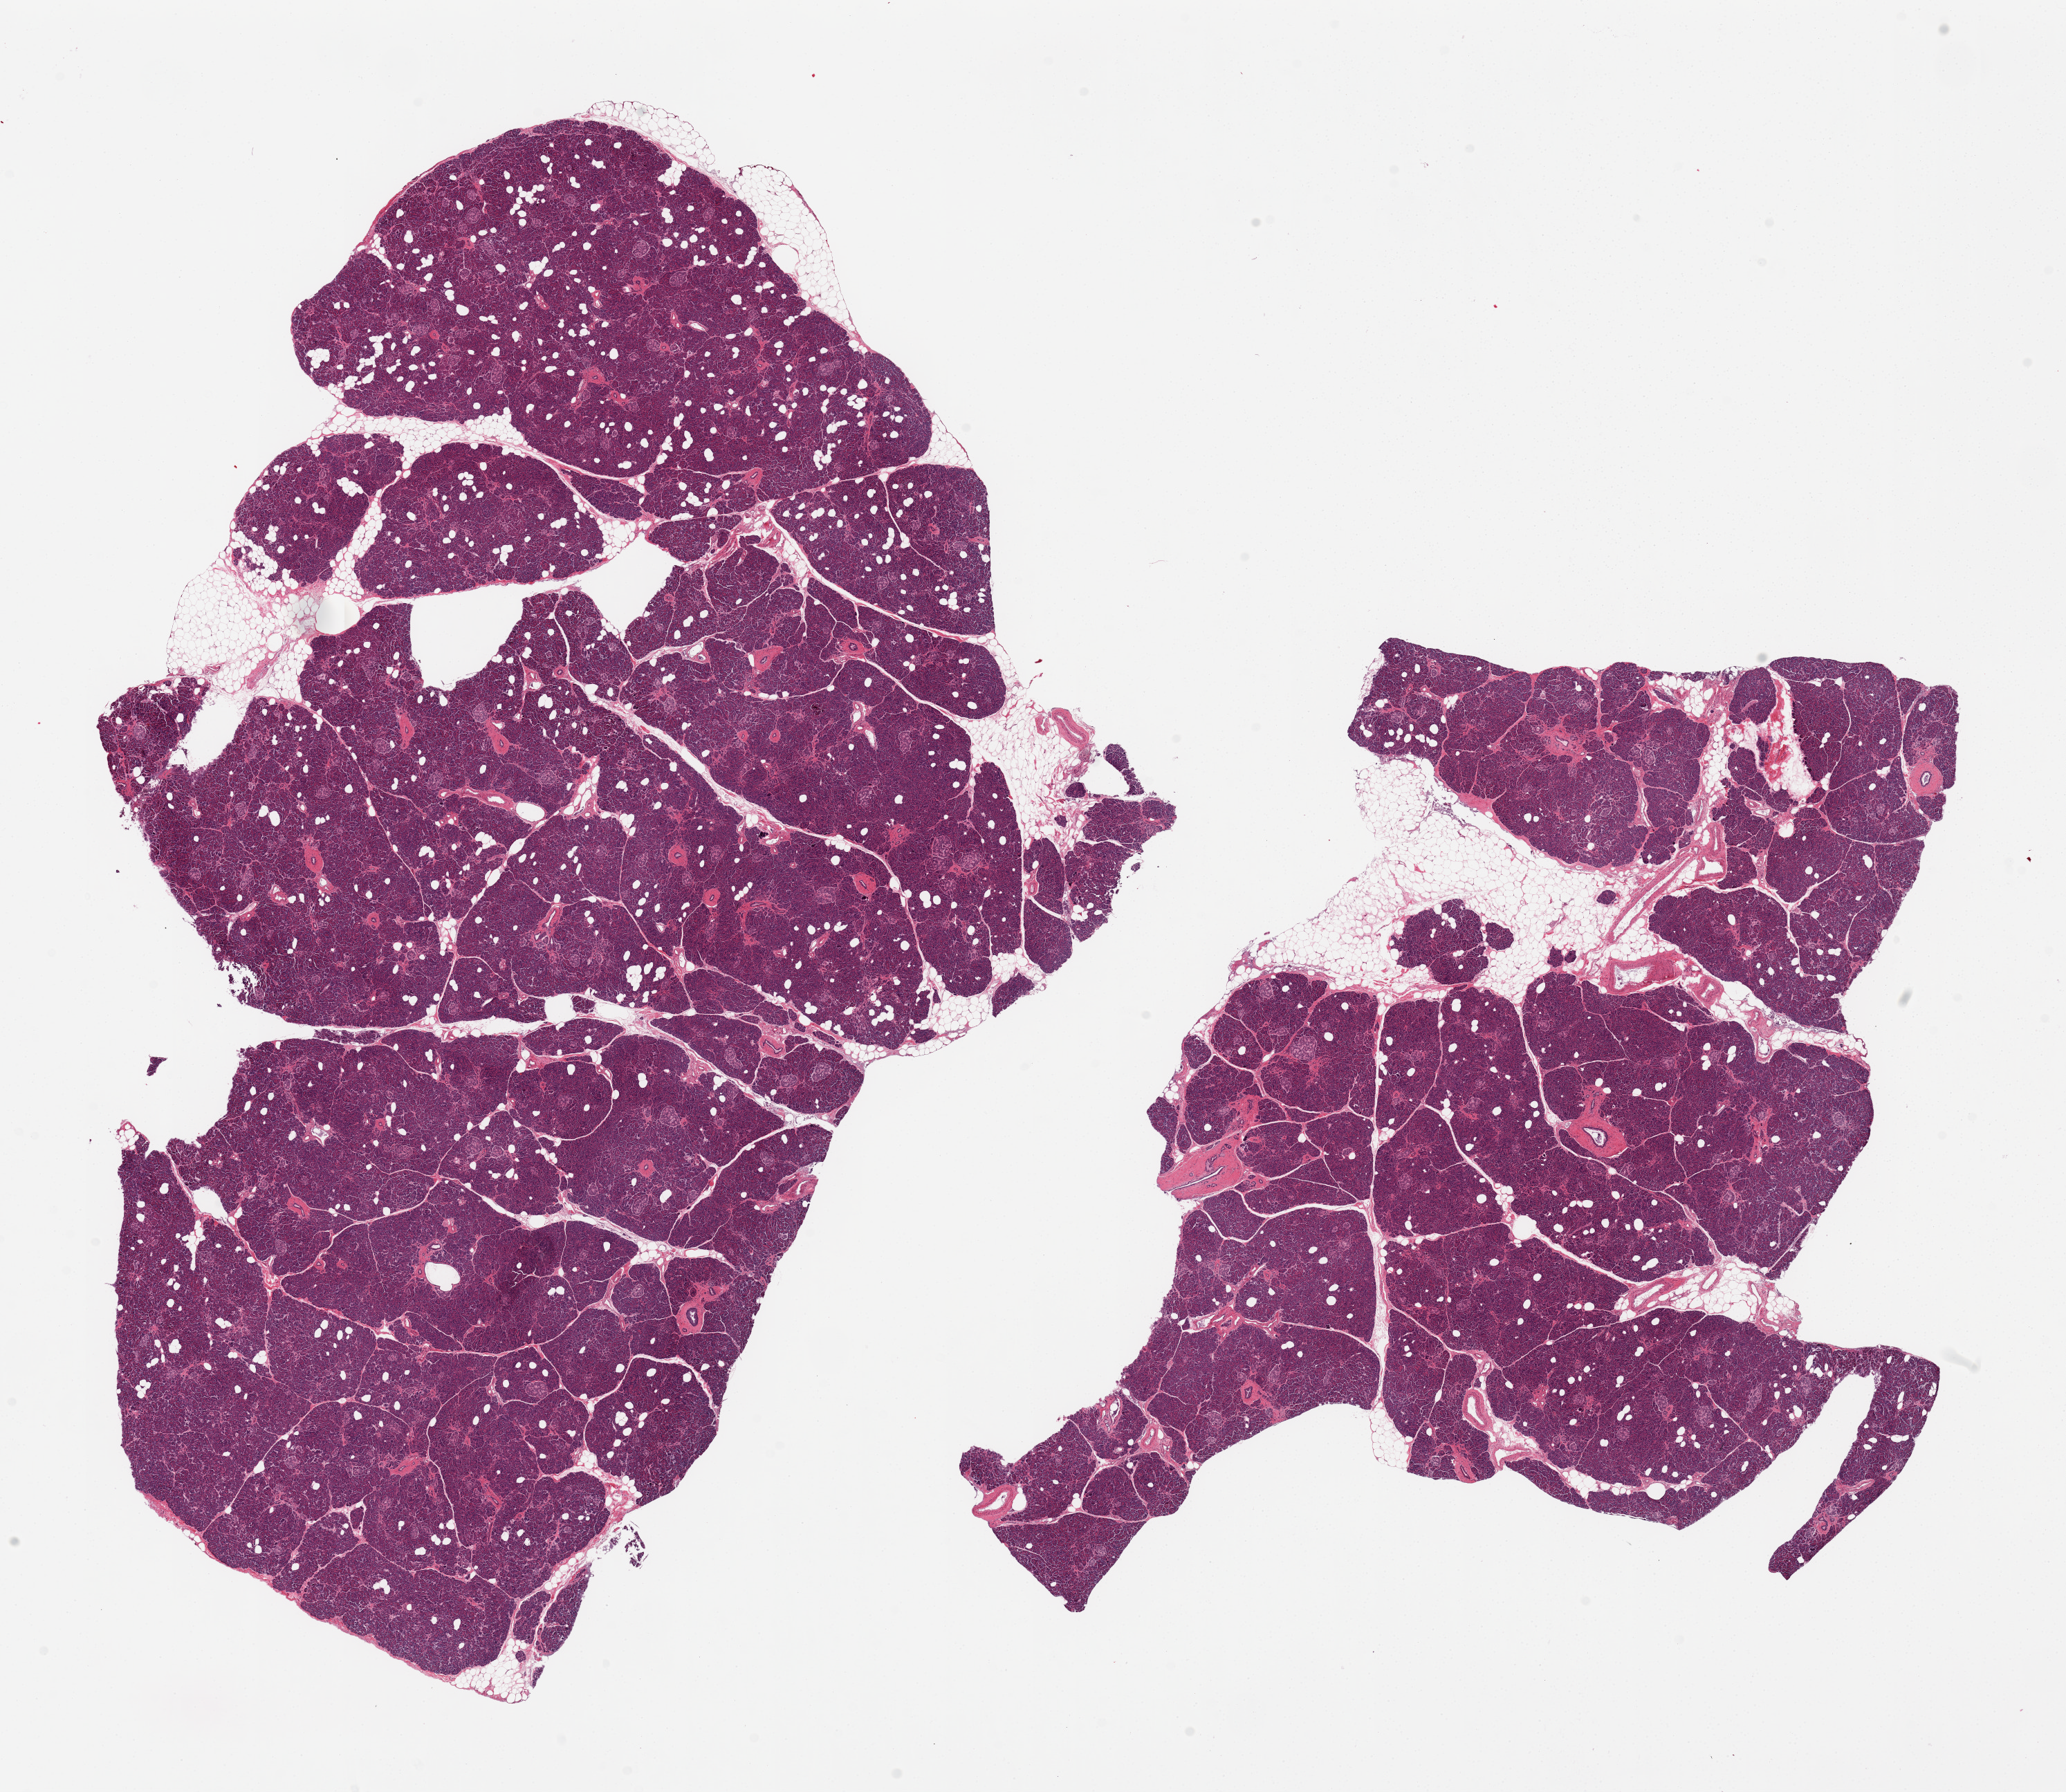
Whole-slide image, haematoxylin and eosin stain — low-resolution overview of the scanned area, about 23.6 x 20.5 mm; PAXgene-fixed paraffin-embedded (PFPE) section; target tissue: pancreas; tissue donor sample. Male donor.
Pathologist's review note for this sample: 2 pieces, 17x11 and 14x8mm; scattered fat cells overall (10%).